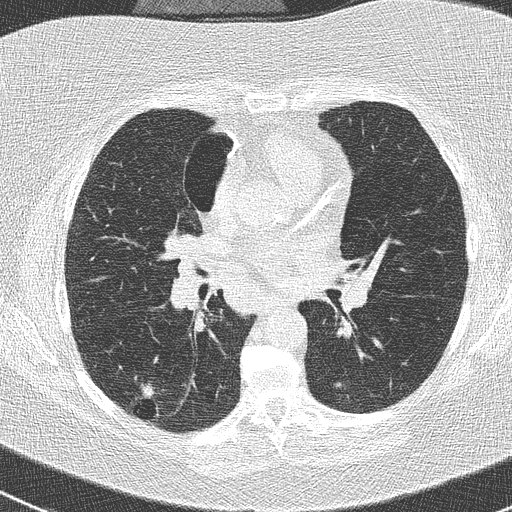
Low-dose screening chest CT, one axial slice; slice 138 of 261 in the series (ordered by position); reconstruction kernel B50f; 120 kVp; lung window (W 1500 / L -600 HU); 512 × 512 image matrix, field of view 310 × 310 mm.
Outlined on this slice (expert manual segmentation):
- lesion 1 (tumor, lower lobe of right lung): bounding box <141,383,155,398> (left, top, right, bottom; pixels)